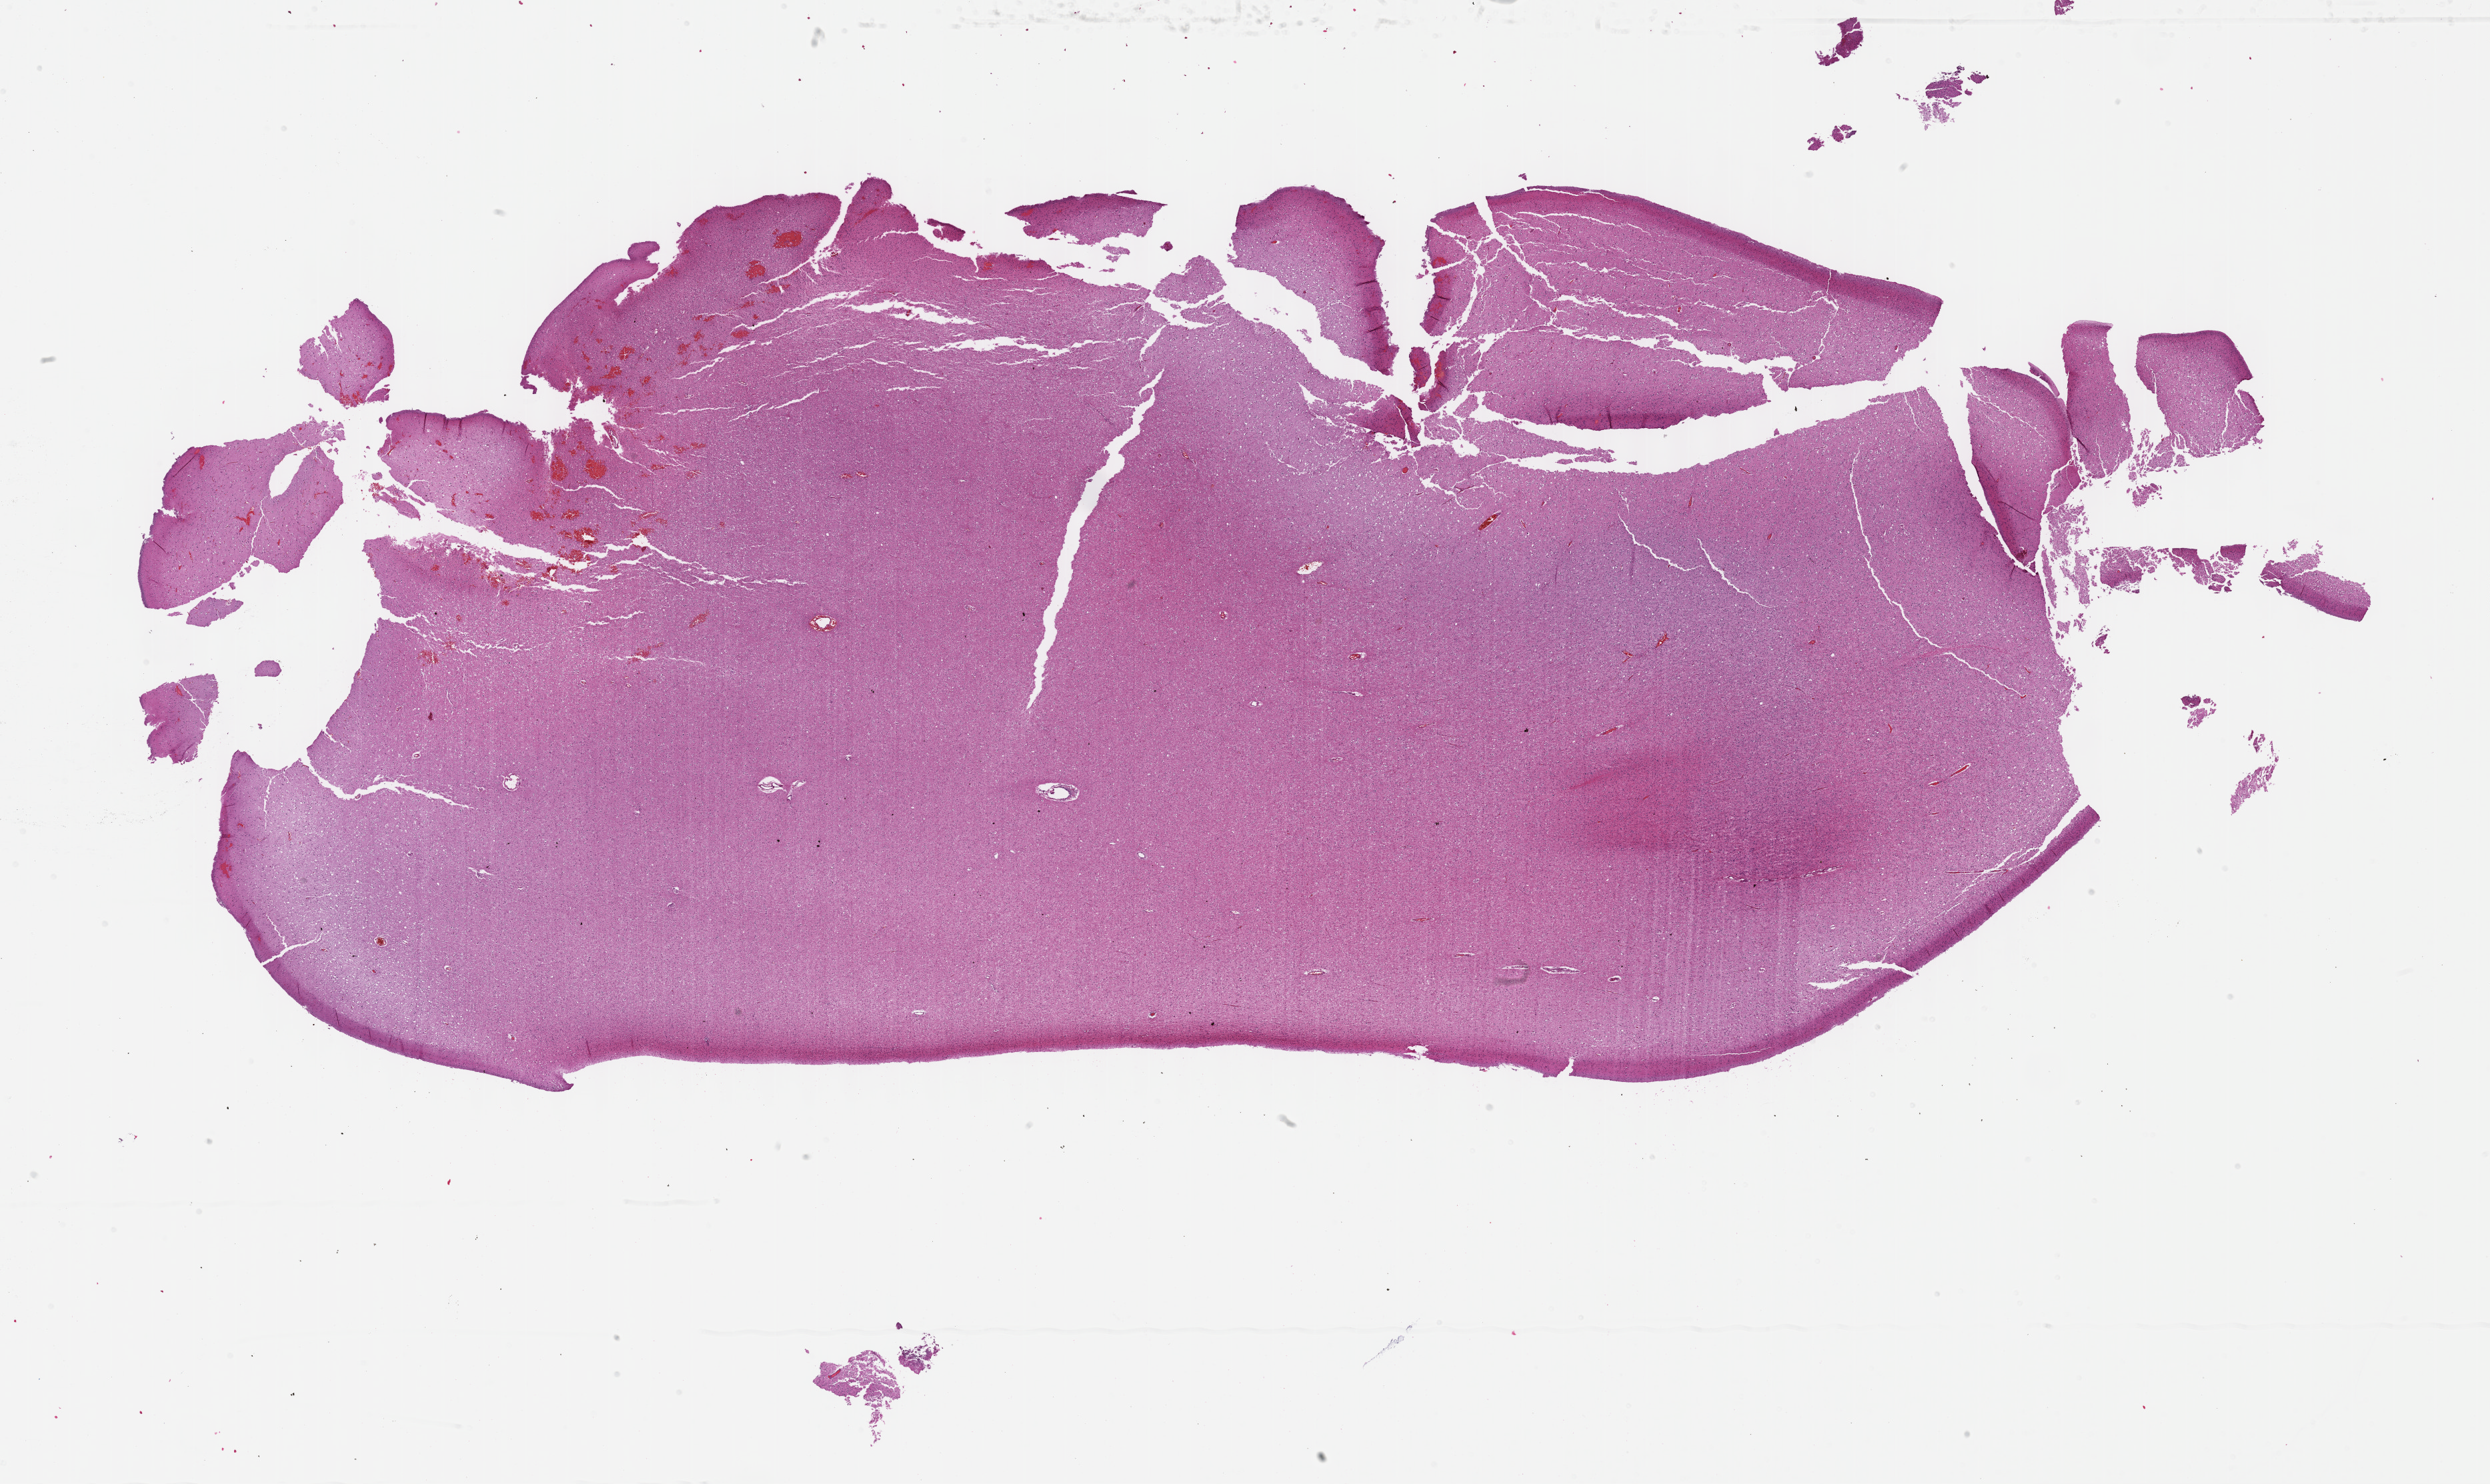
Whole-slide histology image, H&E, low-resolution overview of the scanned area, about 30.2 x 18.0 mm; formalin-fixed paraffin-embedded (FFPE) diagnostic section; brain, primary tumour sample. Male, age 20 years at initial diagnosis. Histologic grade: G2 (moderately differentiated).
Pathologic diagnosis: Astrocytoma, NOS (cerebrum). Laterality: right.